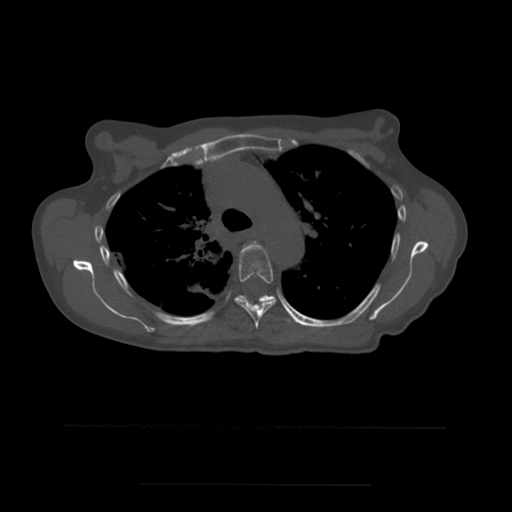
CT including the spine, one axial slice; bone window (W 1800 / L 400 HU); 1.25 mm slice thickness; 512 × 512 image matrix, field of view 350 × 350 mm. Patient age 58 years. Case-level facts recorded for this patient, not image findings: primary cancer: lung.
Outlined on this slice (semi-automatic segmentation, software-assisted and operator-edited):
- T4 vertebra: bounding box (x1, y1, x2, y2) in pixels: (244, 242, 263, 249)
- T5 vertebra: (235, 246, 277, 329)
- T6 vertebra: (236, 295, 294, 322)